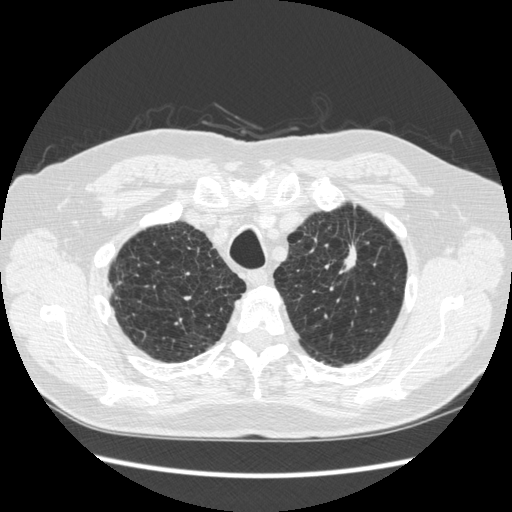
Low-dose screening chest CT, axial slice. Third screening round (two years after baseline). Lung window (W 1500 / L -600 HU). 1.25 mm slice thickness. Standard (soft-tissue) reconstruction kernel (STANDARD). Slice 41 of 267 in the series. Male, age 70 years at enrolment.
Expert-annotated lung lesion, bounding box [x1, y1, x2, y2] px = [323, 222, 375, 287]. The screening reader recorded 2 non-calcified nodules or masses ≥4 mm on this exam (left upper lobe, right lower lobe); which of them this box marks is not recorded.